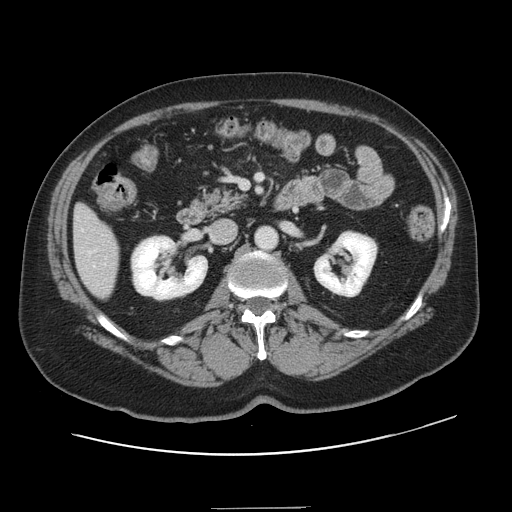
Contrast-enhanced abdominal CT, one axial slice. Position 56 of 143 along the scan axis. Intravenous contrast given. Soft-tissue window (W 400 / L 40 HU). 2.5 mm slice thickness. 512 × 512 image matrix. Male patient, age 62 years. Case-level facts recorded for this patient, not image findings: diagnosis: colorectal cancer liver metastases, imaged before liver resection; multiple liver metastases: yes; largest metastasis: 2.7 cm; disease in both lobes: no.
Annotated regions visible in this slice (manually delineated by an expert):
- hepatic veins: bounding box <89,252,95,267> (left, top, right, bottom; pixels)
- liver: <74,206,118,298>